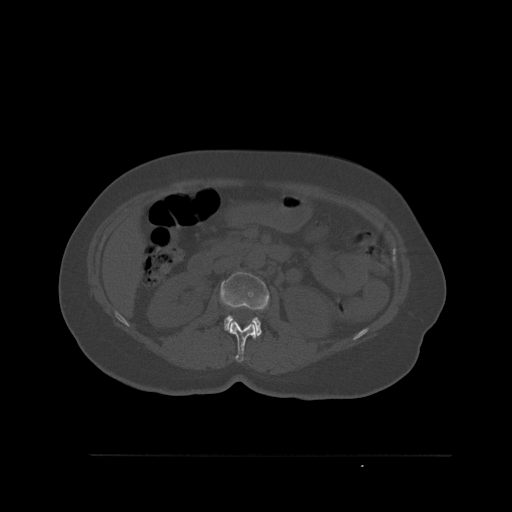
CT including the spine, one axial slice; position 256 of 527 along the scan axis; bone window (W 1800 / L 400 HU); 1.5 mm slice thickness; 512 × 512 image matrix, field of view 470 × 470 mm. Female patient, age 73 years. From the clinical record (not read from this slice): primary cancer: breast.
Structures marked on this image (semi-automatically segmented with operator editing):
- L1 vertebra: bounding box <229,319,257,362> (left, top, right, bottom; pixels)
- L2 vertebra: <220,271,270,337>